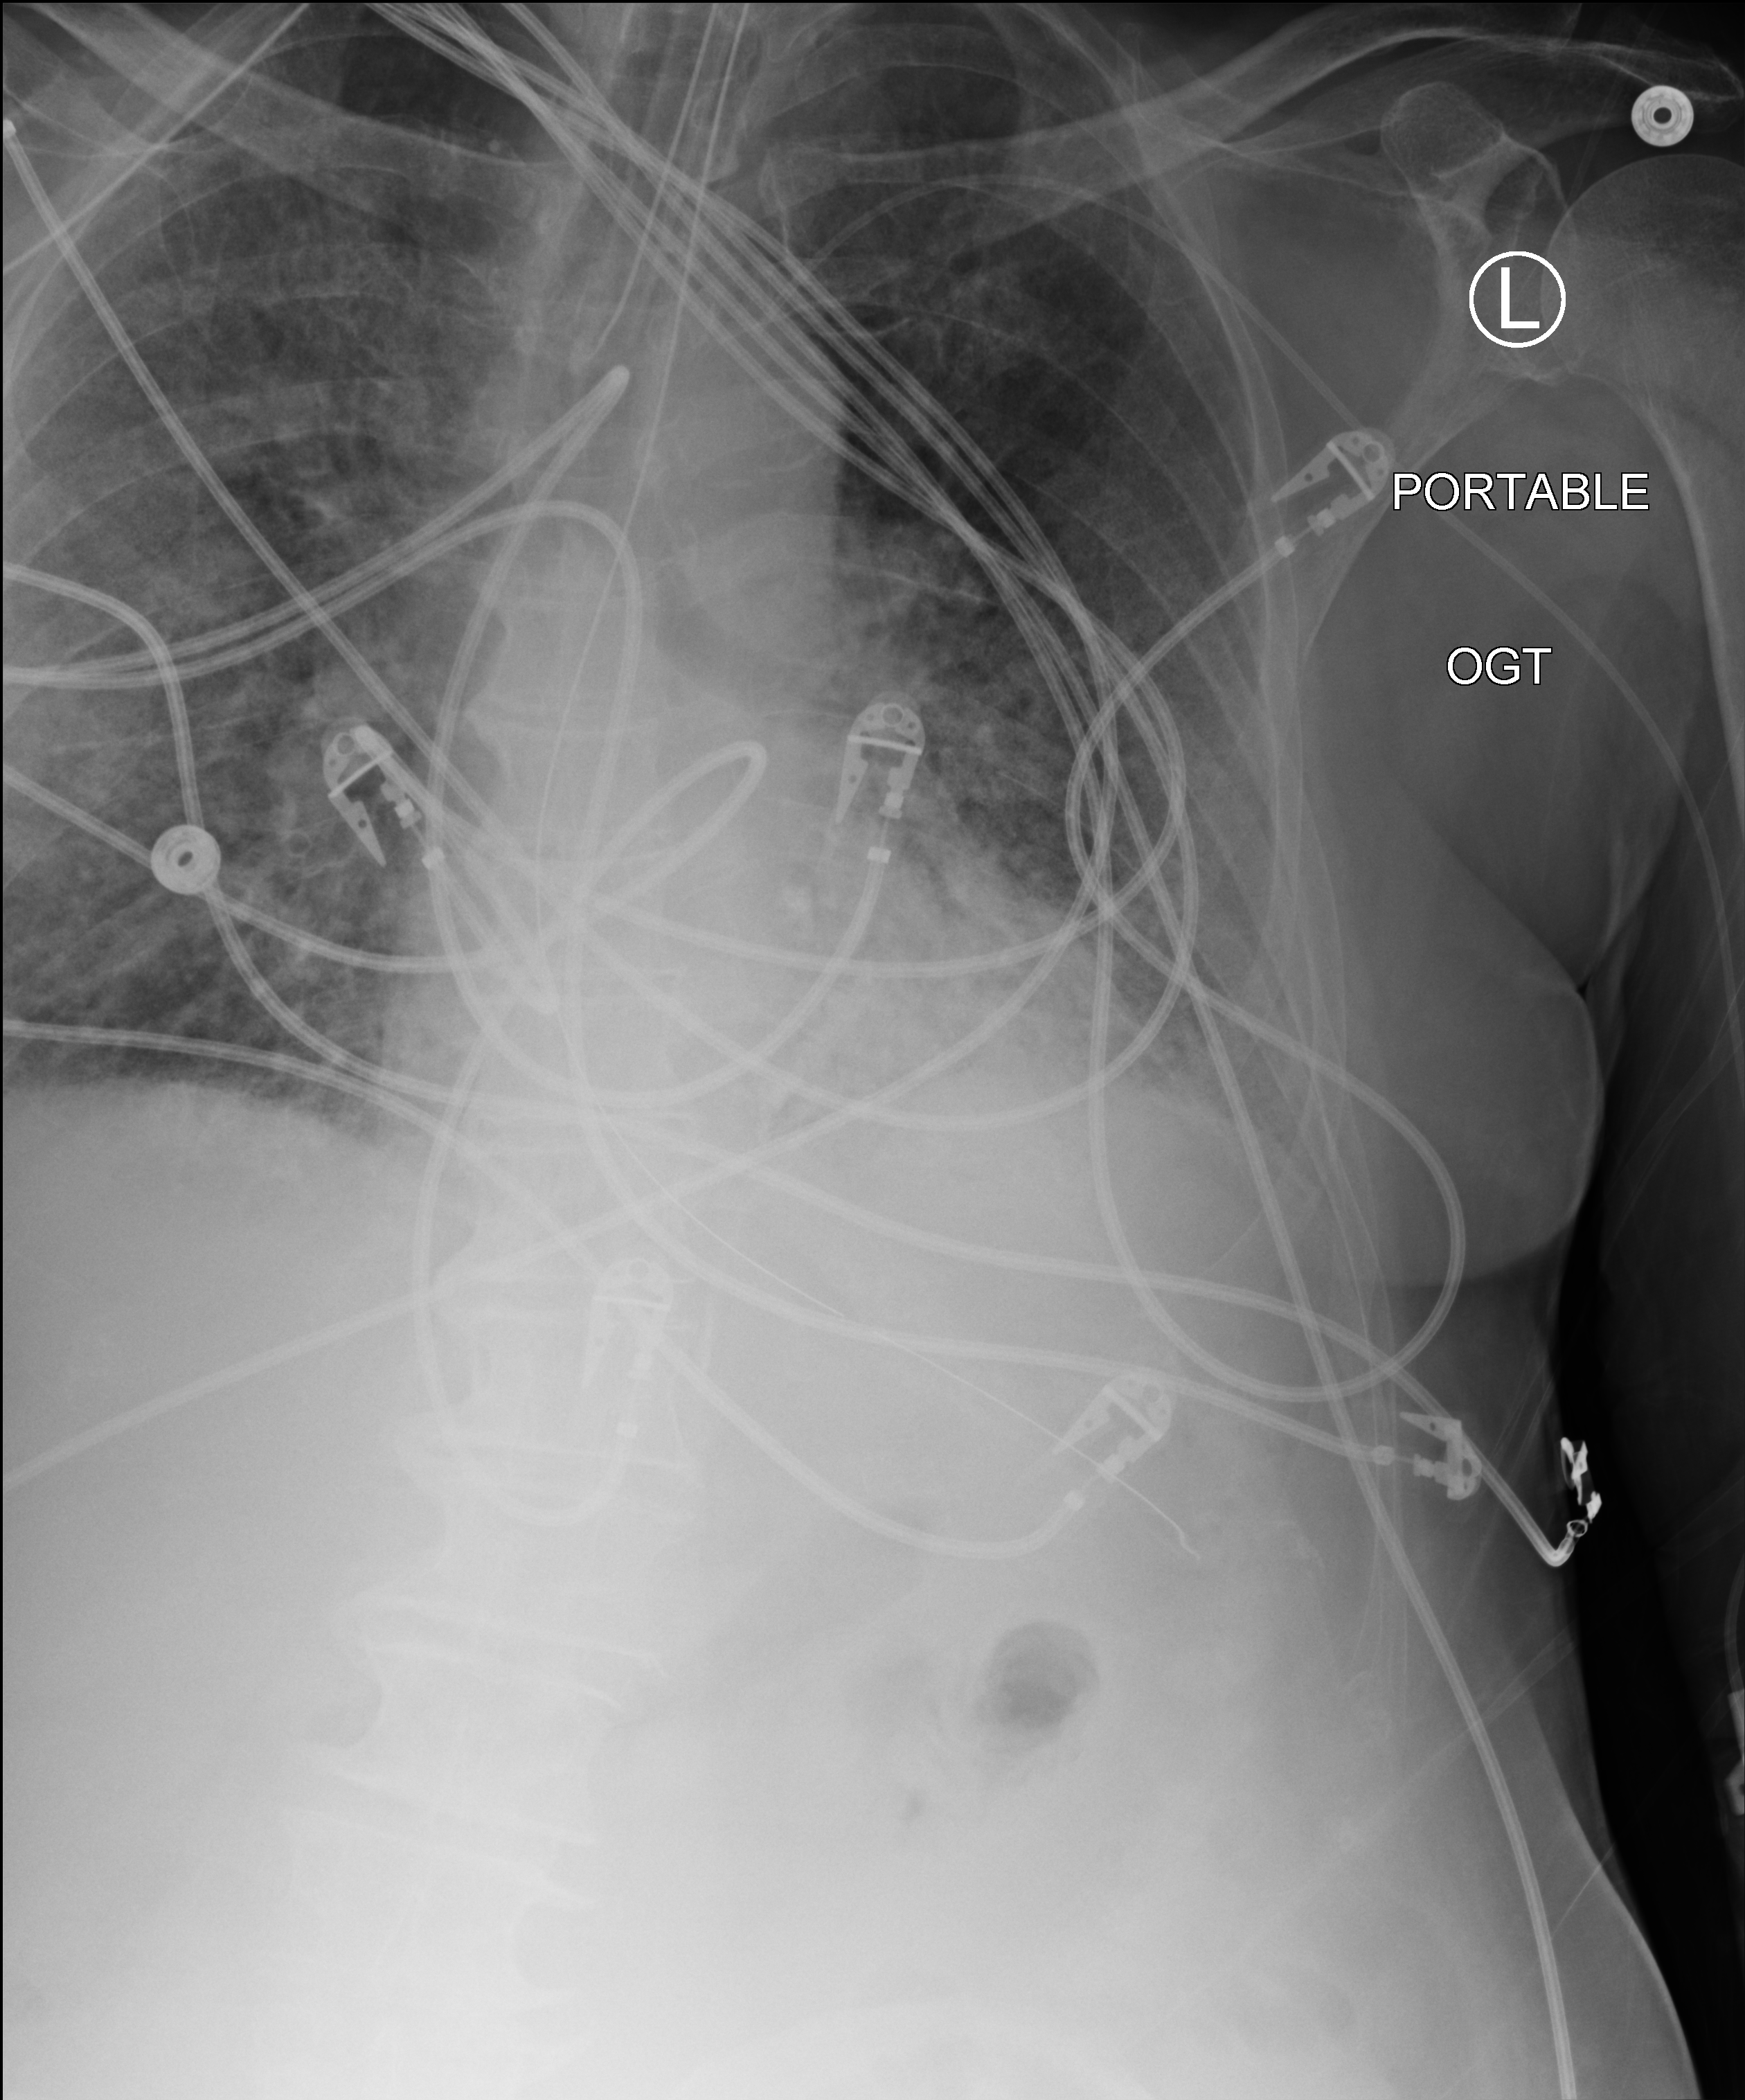
Bedside chest radiograph (computed radiography), anteroposterior (AP) projection. Male patient hospitalised with COVID-19, age 75–90 years.
From the hospital-stay record, not from the radiograph (when in the stay this image was taken is not recorded): diabetes (admission record): no; mechanically ventilated during this hospital stay: yes.